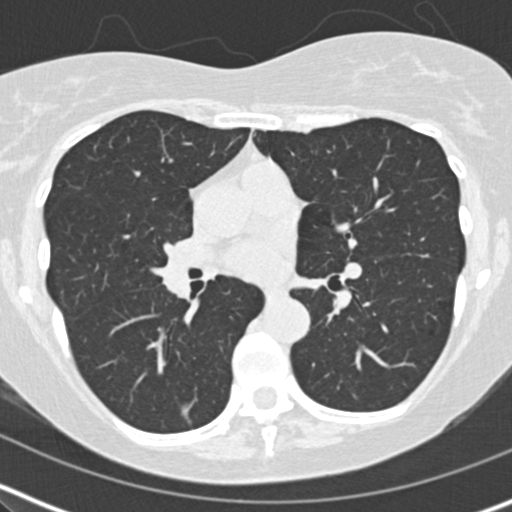
Chest CT (low-dose screening protocol), one axial image; second screening round (one year after baseline); lung window (W 1500 / L -600 HU); 2 mm slice thickness; slice 80 of 164 in the series. Female, age 60 years at enrolment. Former smoker at enrolment.
- Lesion marked by an expert reader, bounding box [x1, y1, x2, y2] px = [165, 387, 221, 438].
- The screening reader recorded 2 non-calcified nodules or masses ≥4 mm on this exam (right middle lobe, right middle lobe); which of them this box marks is not recorded.
- Official screen result: positive, no significant change: stable abnormalities potentially related to lung cancer, unchanged since the prior screening exam.
- Participant outcome: lung cancer diagnosed 453 days after this screen (after the third annual screen) — acinar cell carcinoma, right lower lobe, moderately differentiated (G2), stage IA (AJCC 6th edition), 10 mm at pathology.